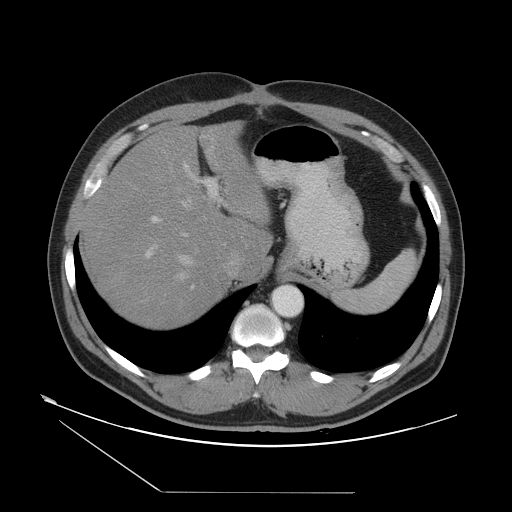
Contrast-enhanced abdominal CT, one axial slice; position 38 of 55 along the scan axis; reconstruction kernel STANDARD; intravenous contrast given; soft-tissue window (W 400 / L 40 HU); 5 mm slice thickness; 512 × 512 image matrix, field of view 454 × 454 mm. Male patient, age 59 years. Case-level facts recorded for this patient, not image findings: diagnosis: colorectal cancer liver metastases, imaged before liver resection; multiple liver metastases: yes; largest metastasis: 0.3 cm.
Structures marked on this image (expert manual segmentation):
- hepatic veins: bounding box <176,184,225,280> (left, top, right, bottom; pixels)
- liver: <84,126,270,326>
- planned liver remnant (the part of the liver to remain after resection): <85,149,268,326>
- portal vein (with intrahepatic branches): <145,163,217,289>